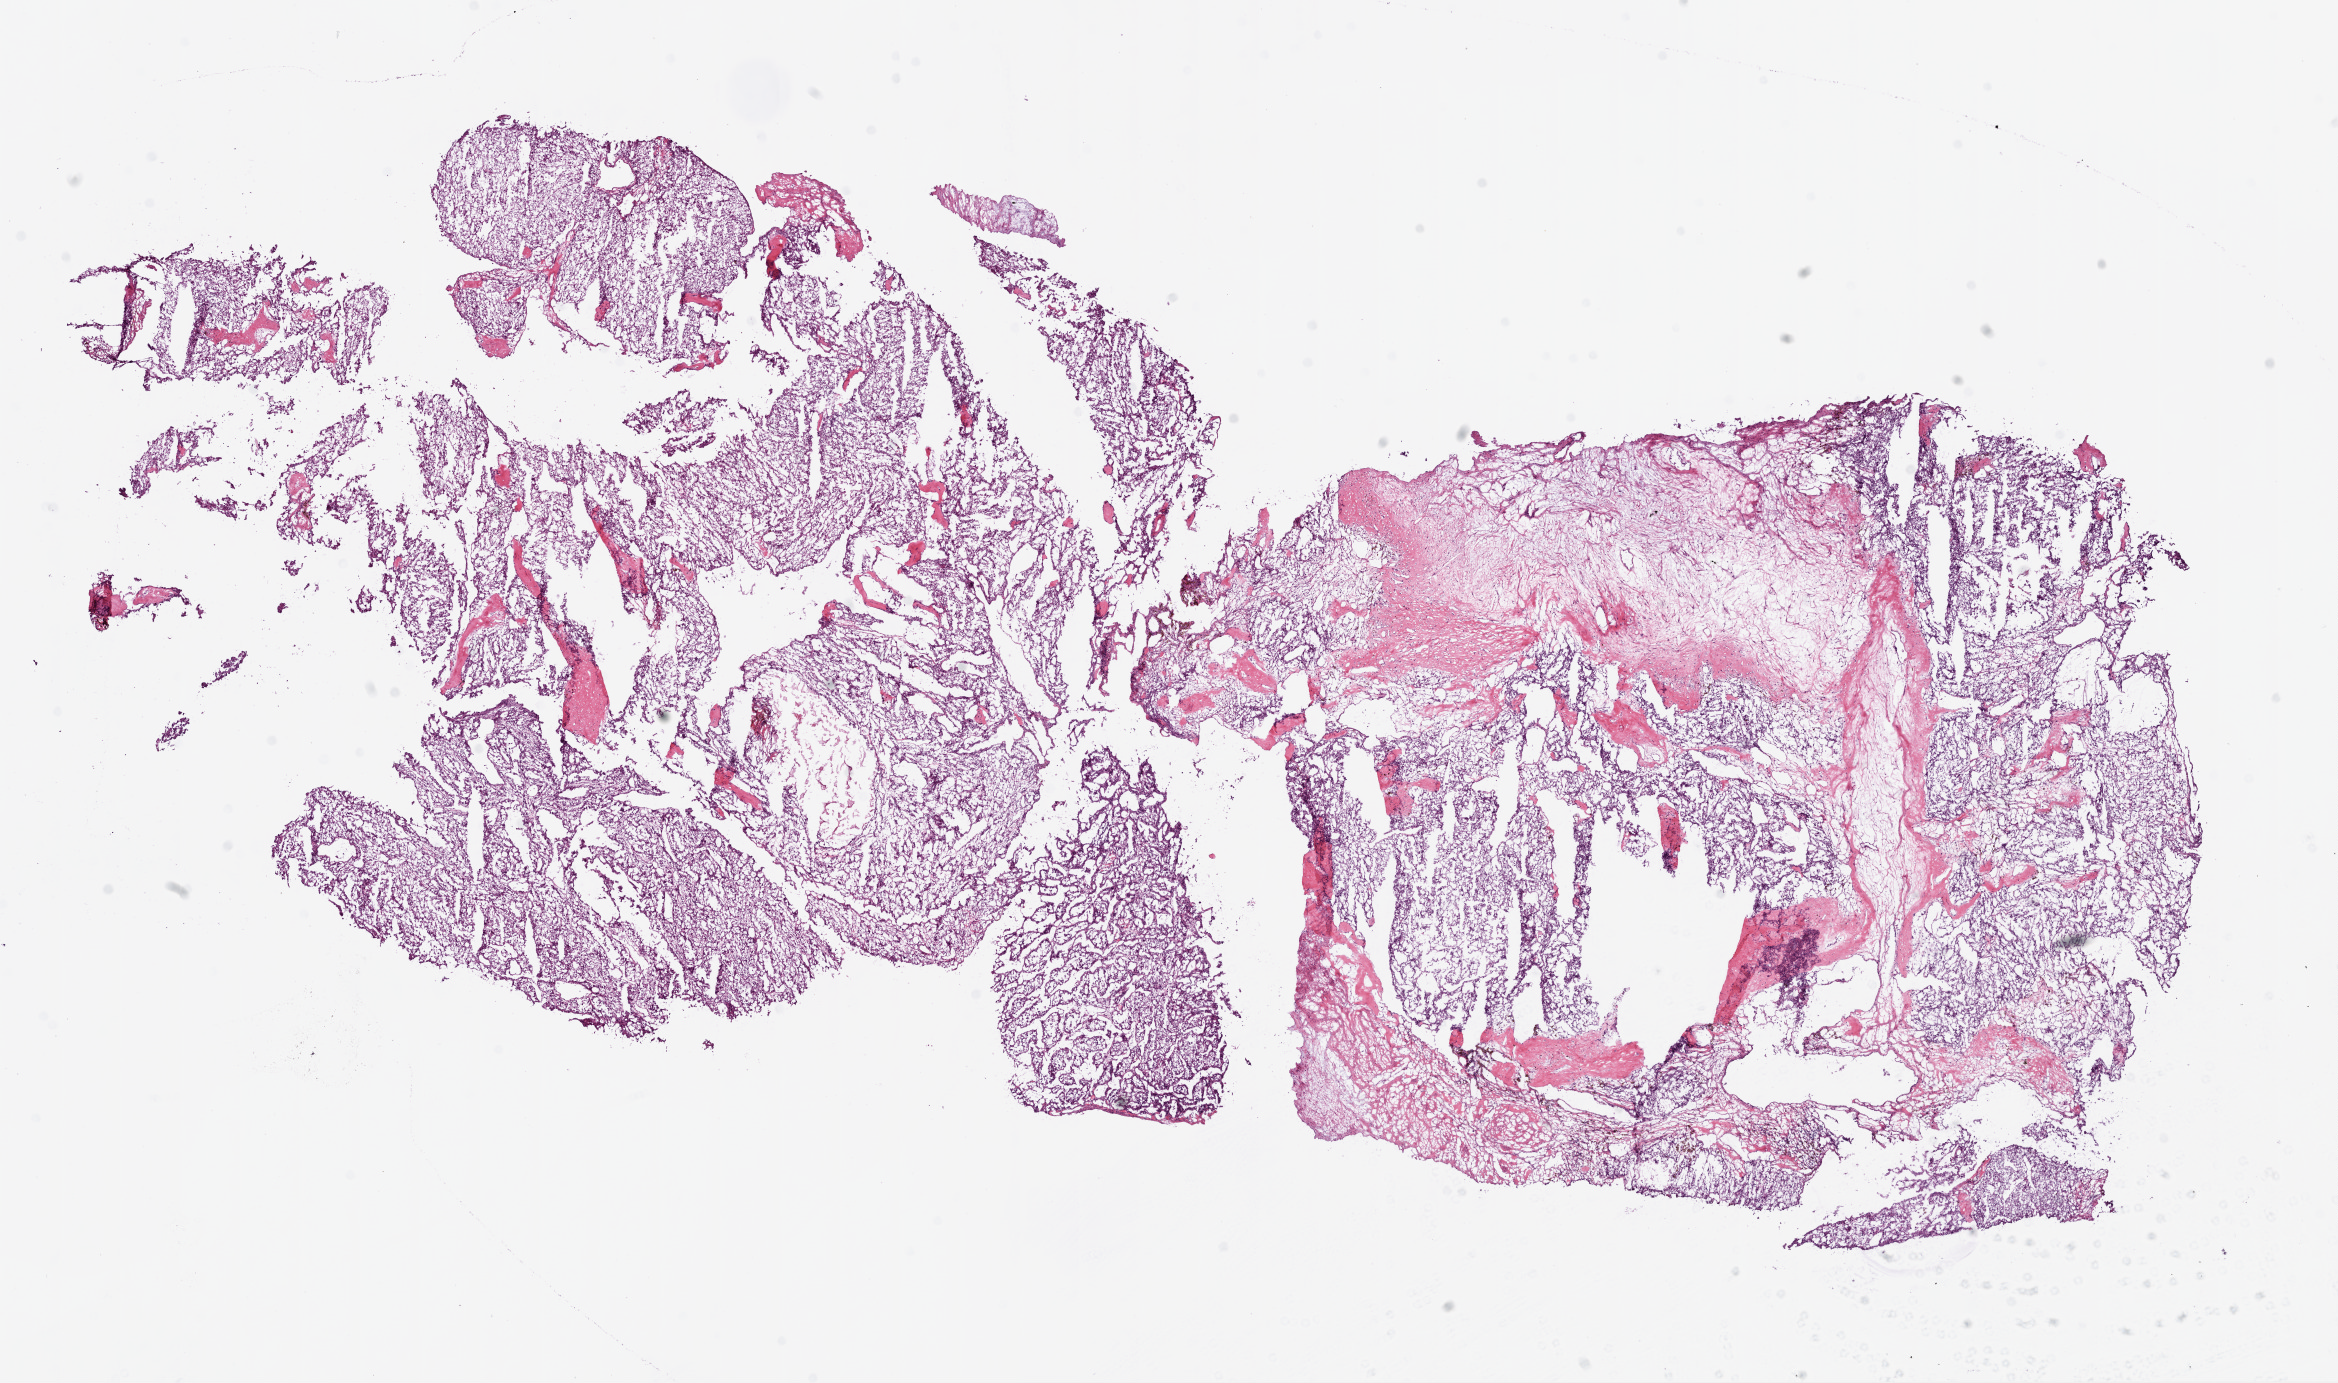
Hematoxylin and eosin (H&E) stained whole-slide image — whole scanned area (about 18.9 x 11.2 mm, slide scanned at 20x) shown as a low-resolution overview. Frozen section. Primary tumour sample from the kidney. Male patient; age at initial diagnosis 47 years. Pathologist review of this section (percent, as recorded): tumour cells 82%, tumour nuclei 85%.
Histologic diagnosis: Clear cell adenocarcinoma, NOS.